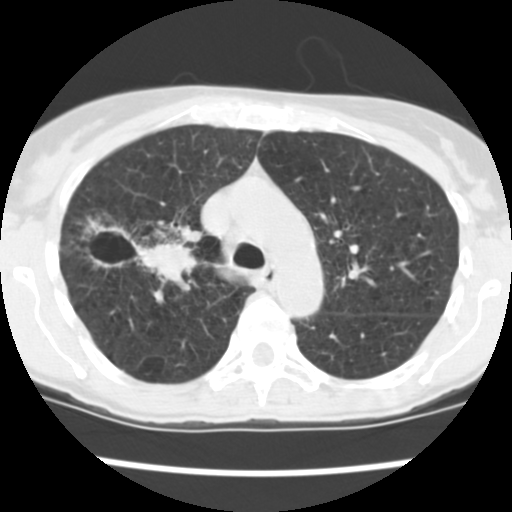
Chest CT (low-dose screening protocol), one axial image; first (baseline) screen; lung window (W 1500 / L -600 HU). Female, age 60 years at enrolment. Current smoker at enrolment.
Lesion marked by an expert reader, box from (x=84, y=216) to (x=197, y=285) px. The screening reader recorded 3 non-calcified nodules or masses ≥4 mm on this exam (right upper lobe, right upper lobe, right lower lobe); which of them this box marks is not recorded. Later outcome: lung cancer diagnosed 19 days after this screen — non-small cell carcinoma, right upper lobe, stage IV (AJCC 6th edition), 26 mm at pathology.